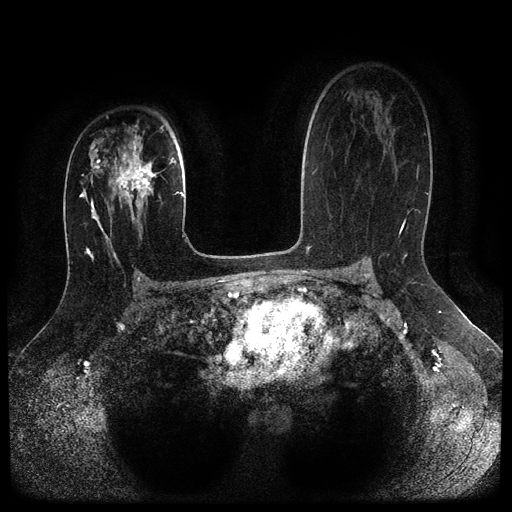
Breast MRI (dynamic contrast-enhanced, multi-phase), one axial slice; position 65 of 116 along the scan axis; dynamic contrast-enhanced series, time point 2 of 5 at this slice position (early post-contrast); 1.5 T; TE 2.6 ms, TR 5.4 ms; 2 mm slice thickness; 512 × 512 image matrix, field of view 340 × 340 mm. Patient: female, 29 years.
Annotated regions visible in this slice (semi-automatically segmented with operator editing):
- breast lesion (labelled 'tumour' in the annotation; benign lesions carry a separate 'benign' label): bounding box (x1, y1, x2, y2) in pixels: (108, 135, 164, 205)